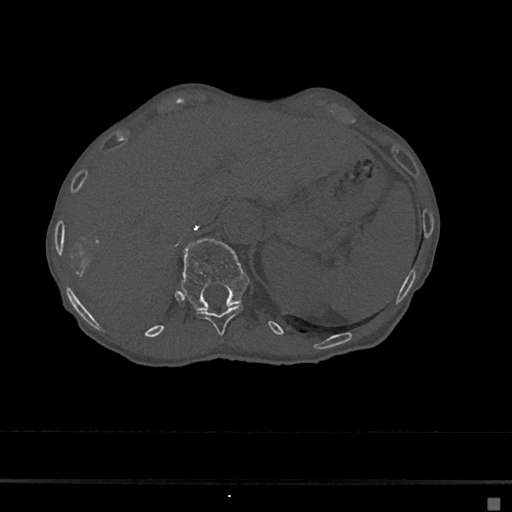
CT including the spine, one axial slice. Position 145 of 797 along the scan axis. Reconstruction kernel Br40s/3. 120 kVp. Bone window (W 1800 / L 400 HU). 512 × 512 image matrix, field of view 360 × 360 mm. Female patient, age 68 years. From the clinical record (not read from this slice): primary cancer: renal.
Annotated regions visible in this slice (semi-automatic segmentation, software-assisted and operator-edited):
- T11 vertebra: bounding box (x1, y1, x2, y2) in pixels: (195, 304, 244, 335)
- T12 vertebra: (181, 239, 250, 311)